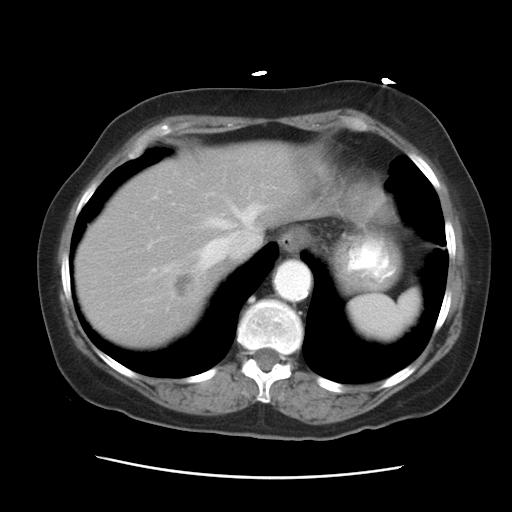
Contrast-enhanced abdominal CT, one axial slice; position 24 of 29 along the scan axis; reconstruction kernel STANDARD; 120 kVp; intravenous contrast given; soft-tissue window (W 400 / L 40 HU); 7.5 mm slice thickness; 512 × 512 image matrix, field of view 354 × 354 mm. Female patient, age 64 years. Case-level facts recorded for this patient, not image findings: diagnosis: colorectal cancer liver metastases, imaged before liver resection; multiple liver metastases: no; largest metastasis: 2.5 cm; disease in both lobes: no.
Annotated regions visible in this slice (outlined manually by an expert reader):
- hepatic veins: bounding box [x1, y1, x2, y2] px = [152, 194, 263, 273]
- liver: [76, 147, 316, 346]
- planned liver remnant (the part of the liver to remain after resection): [76, 147, 315, 271]
- liver metastasis: [171, 272, 198, 298]